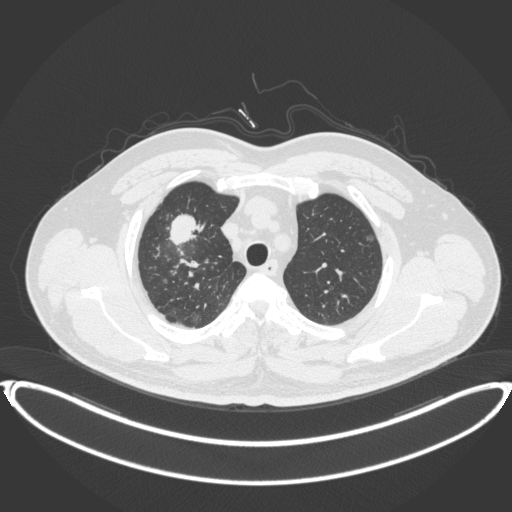
Chest CT, one axial slice. Slice 312 of 399 in the series (ordered by position). Reconstruction kernel B31f. Lung window (W 1500 / L -600 HU). 512 × 512 image matrix. Male patient, age 53 years. From the clinical record (not read from this slice): clinical TNM (as recorded): T2a N0 M0.
Annotated regions visible in this slice (bounding box drawn by a radiologist):
- lung tumour (recorded histology: adenocarcinoma): bounding box [x1, y1, x2, y2] px = [164, 207, 208, 249]